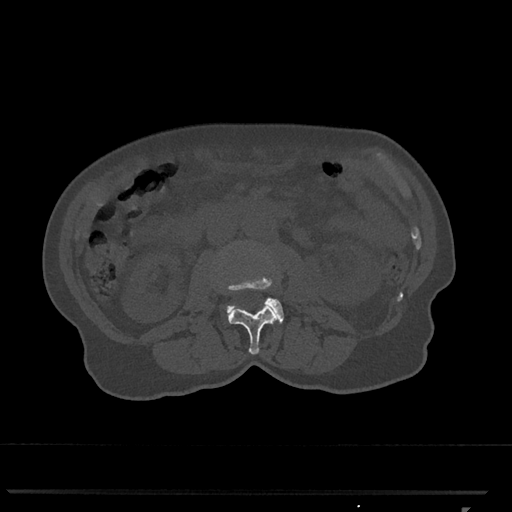
CT including the spine, one axial slice. Slice 308 of 793 in the series (ordered by position). 120 kVp. Bone window (W 1800 / L 400 HU). 512 × 512 image matrix, field of view 380 × 380 mm. Female patient, age 62 years. Case-level facts recorded for this patient, not image findings: primary cancer: renal.
Annotated regions visible in this slice (semi-automatic segmentation, software-assisted and operator-edited):
- L2 vertebra: bounding box (x1, y1, x2, y2) in pixels: (227, 303, 278, 355)
- L3 vertebra: (226, 277, 284, 323)